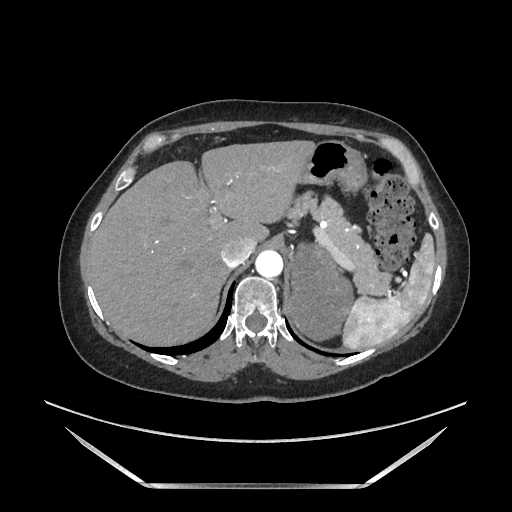
Contrast-enhanced abdominal CT, one axial slice; slice 137 of 205 in the series (ordered by position); soft-tissue window (W 400 / L 40 HU); 1.25 mm slice thickness; 512 × 512 image matrix, field of view 440 × 440 mm. Female patient. Case-level facts recorded for this patient, not image findings: diagnosis: adrenocortical carcinoma; tumour side: left adrenal; tumour size at pathology: 12.5 cm; Ki-67 index: 39 %; stage (as recorded): 3.
Annotated regions visible in this slice (semi-automatic segmentation, software-assisted and operator-edited):
- mass: bounding box (x1, y1, x2, y2) in pixels: (291, 245, 352, 340)